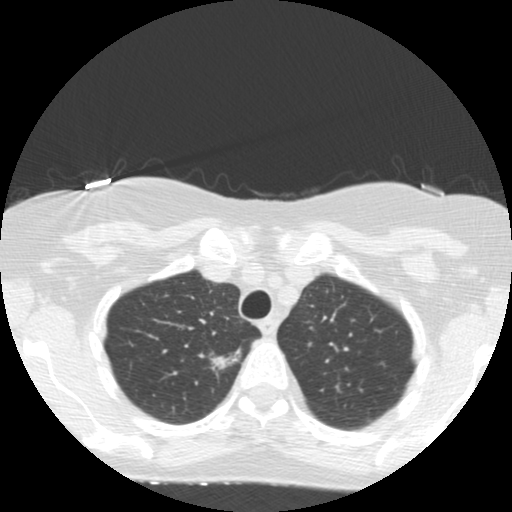
Low-dose screening chest CT, one axial slice. Slice 124 of 155 in the series (ordered by position). Reconstruction kernel STANDARD. 120 kVp. Lung window (W 1500 / L -600 HU). 512 × 512 image matrix, field of view 300 × 300 mm.
Structures marked on this image (manually delineated by an expert):
- lesion 1 (tumor, upper lobe of right lung): bounding box (x1, y1, x2, y2) in pixels: (210, 348, 241, 370)